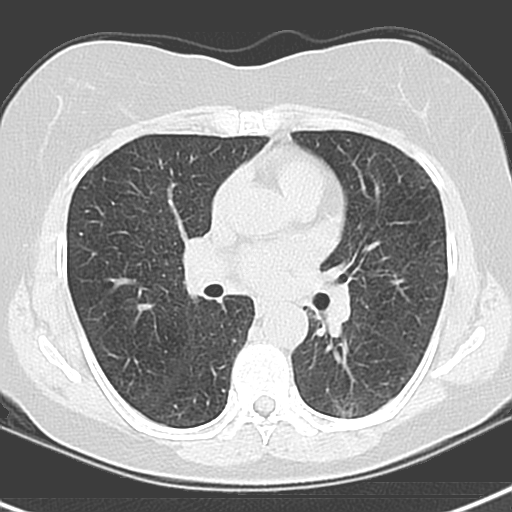
Low-dose screening chest CT, axial slice. Baseline screening round. Lung window (W 1500 / L -600 HU). 3.2 mm slice thickness. Standard (soft-tissue) reconstruction kernel (B). 512 × 512 image matrix, field of view 290 × 290 mm. Female participant, aged 55 years at enrolment. Current smoker at enrolment.
Lesion marked by an expert reader, box from (x=304, y=373) to (x=382, y=424) px. The screening reader recorded 3 non-calcified nodules or masses ≥4 mm on this exam; which of them this box marks is not recorded. Official screen result: positive, change unspecified: nodule(s) >= 4 mm or enlarging nodule(s), mass(es), or other non-specific abnormalities suspicious for lung cancer. Lung cancer was diagnosed 1063 days after this screen: adenocarcinoma with mixed subtypes, left lower lobe, poorly differentiated (G3), stage IA (AJCC 6th edition), 21 mm at pathology.